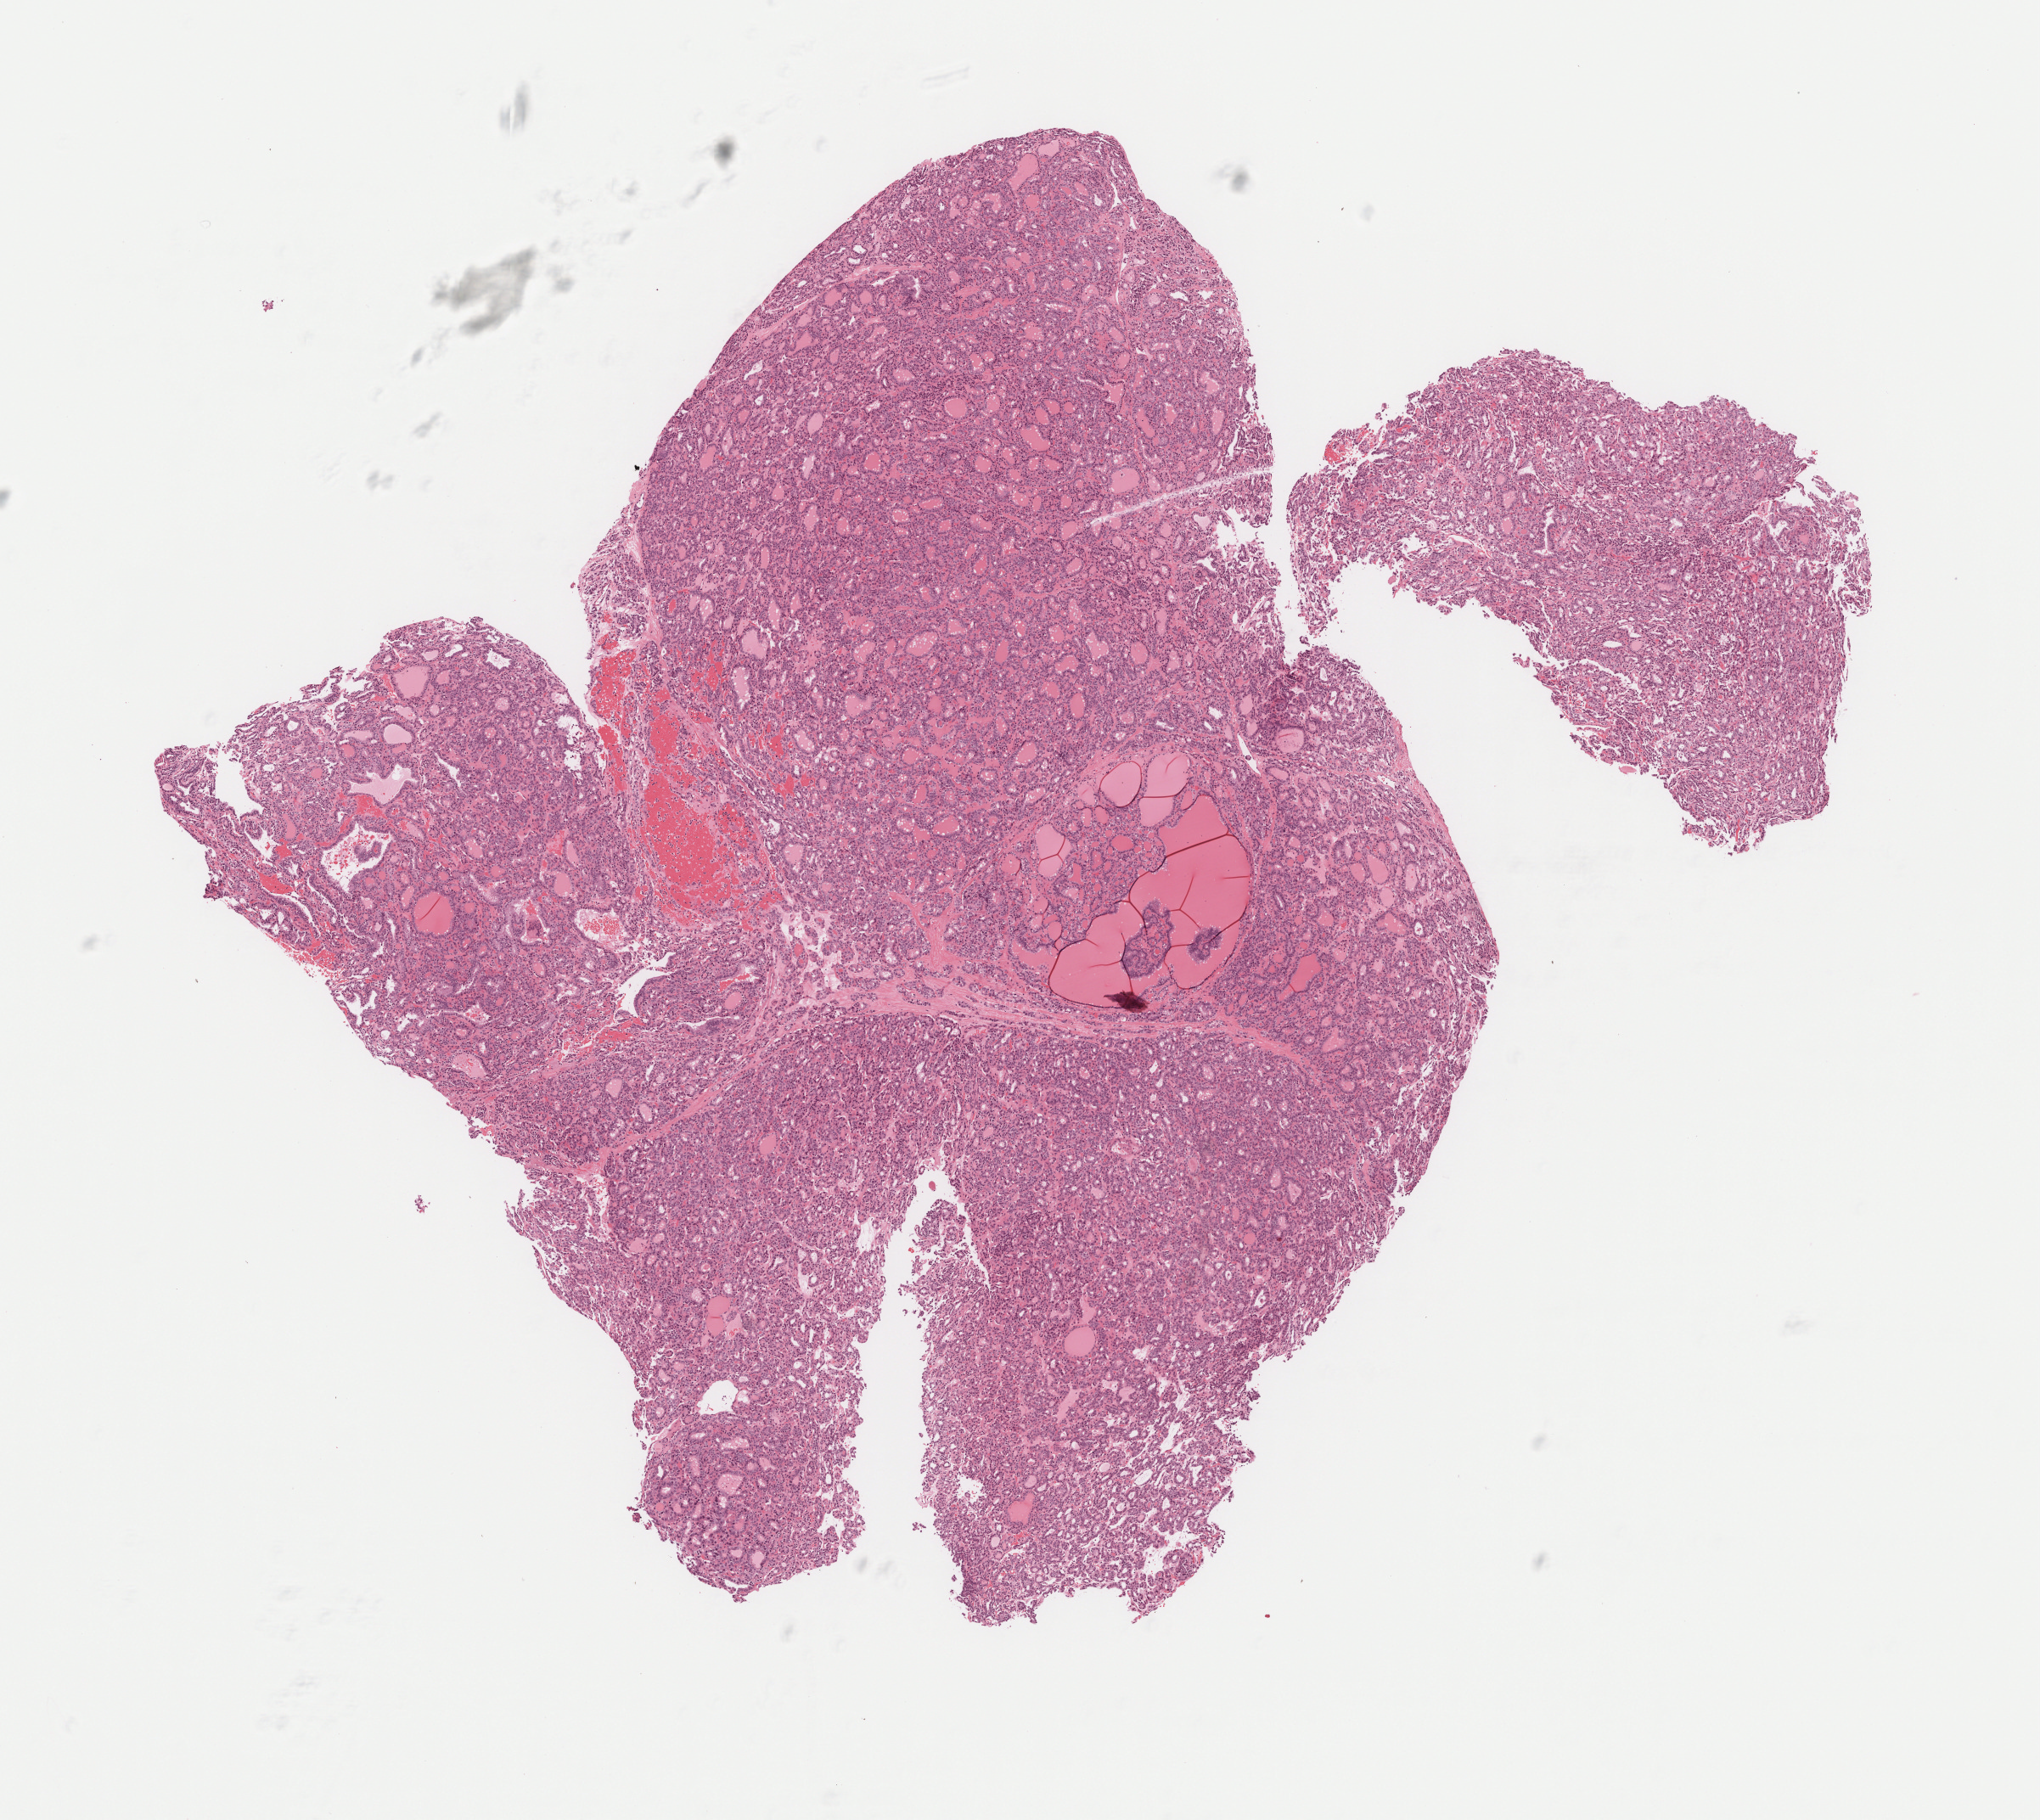
H&E whole-slide image, a low-resolution overview of the entire scanned area, about 9.7 x 8.6 mm (from a 40x scan). Formalin-fixed paraffin-embedded (FFPE) diagnostic section. Thyroid, primary tumour sample. Female, age 46 years at initial diagnosis.
- lymph nodes positive (case pathology): 10 of 83 examined
- diagnosis: Papillary adenocarcinoma, NOS (thyroid gland)
- AJCC pathologic stage: IVA